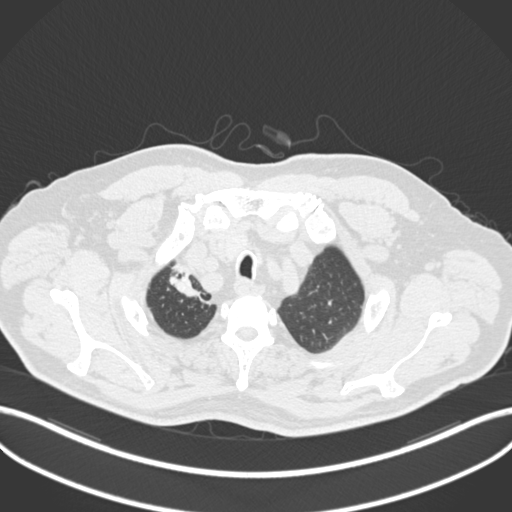
Chest CT, one axial slice. Position 182 of 255 along the scan axis. 120 kVp. Lung window (W 1500 / L -600 HU). 512 × 512 image matrix, field of view 400 × 400 mm. Patient: male, 60 years. From the clinical record (not read from this slice): clinical TNM (as recorded): T1b N1 M0.
Structures marked on this image (rectangle marked by the reading radiologist):
- lung tumour (recorded histology: squamous cell carcinoma): bounding box <158,266,207,307> (left, top, right, bottom; pixels)